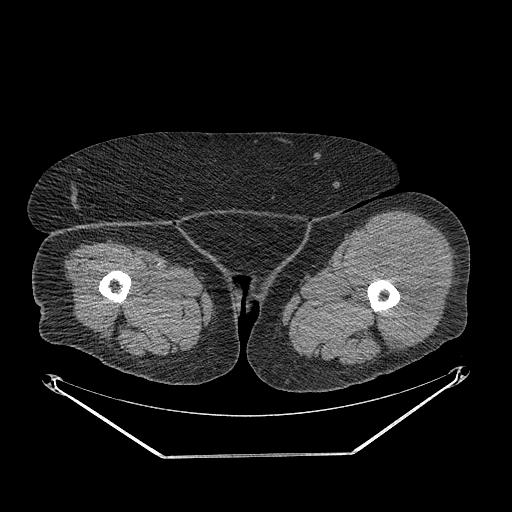
CT of an extremity soft-tissue mass (from a PET/CT study), one axial slice. Slice 243 of 267 in the series (ordered by position). Soft-tissue window (W 400 / L 40 HU). 3.75 mm slice thickness. 512 × 512 image matrix, field of view 500 × 500 mm. Female patient. From the clinical record (not read from this slice): histological type: undifferentiated – high grade; grade: high; site of the primary tumour: left thigh.
Structures marked on this image (expert contour drawn on MRI and transferred to this co-registered scan by the dataset authors):
- gross tumour volume including surrounding oedema: bounding box (x1, y1, x2, y2) in pixels: (354, 231, 439, 350)
- gross tumour volume (mass): (356, 233, 439, 350)